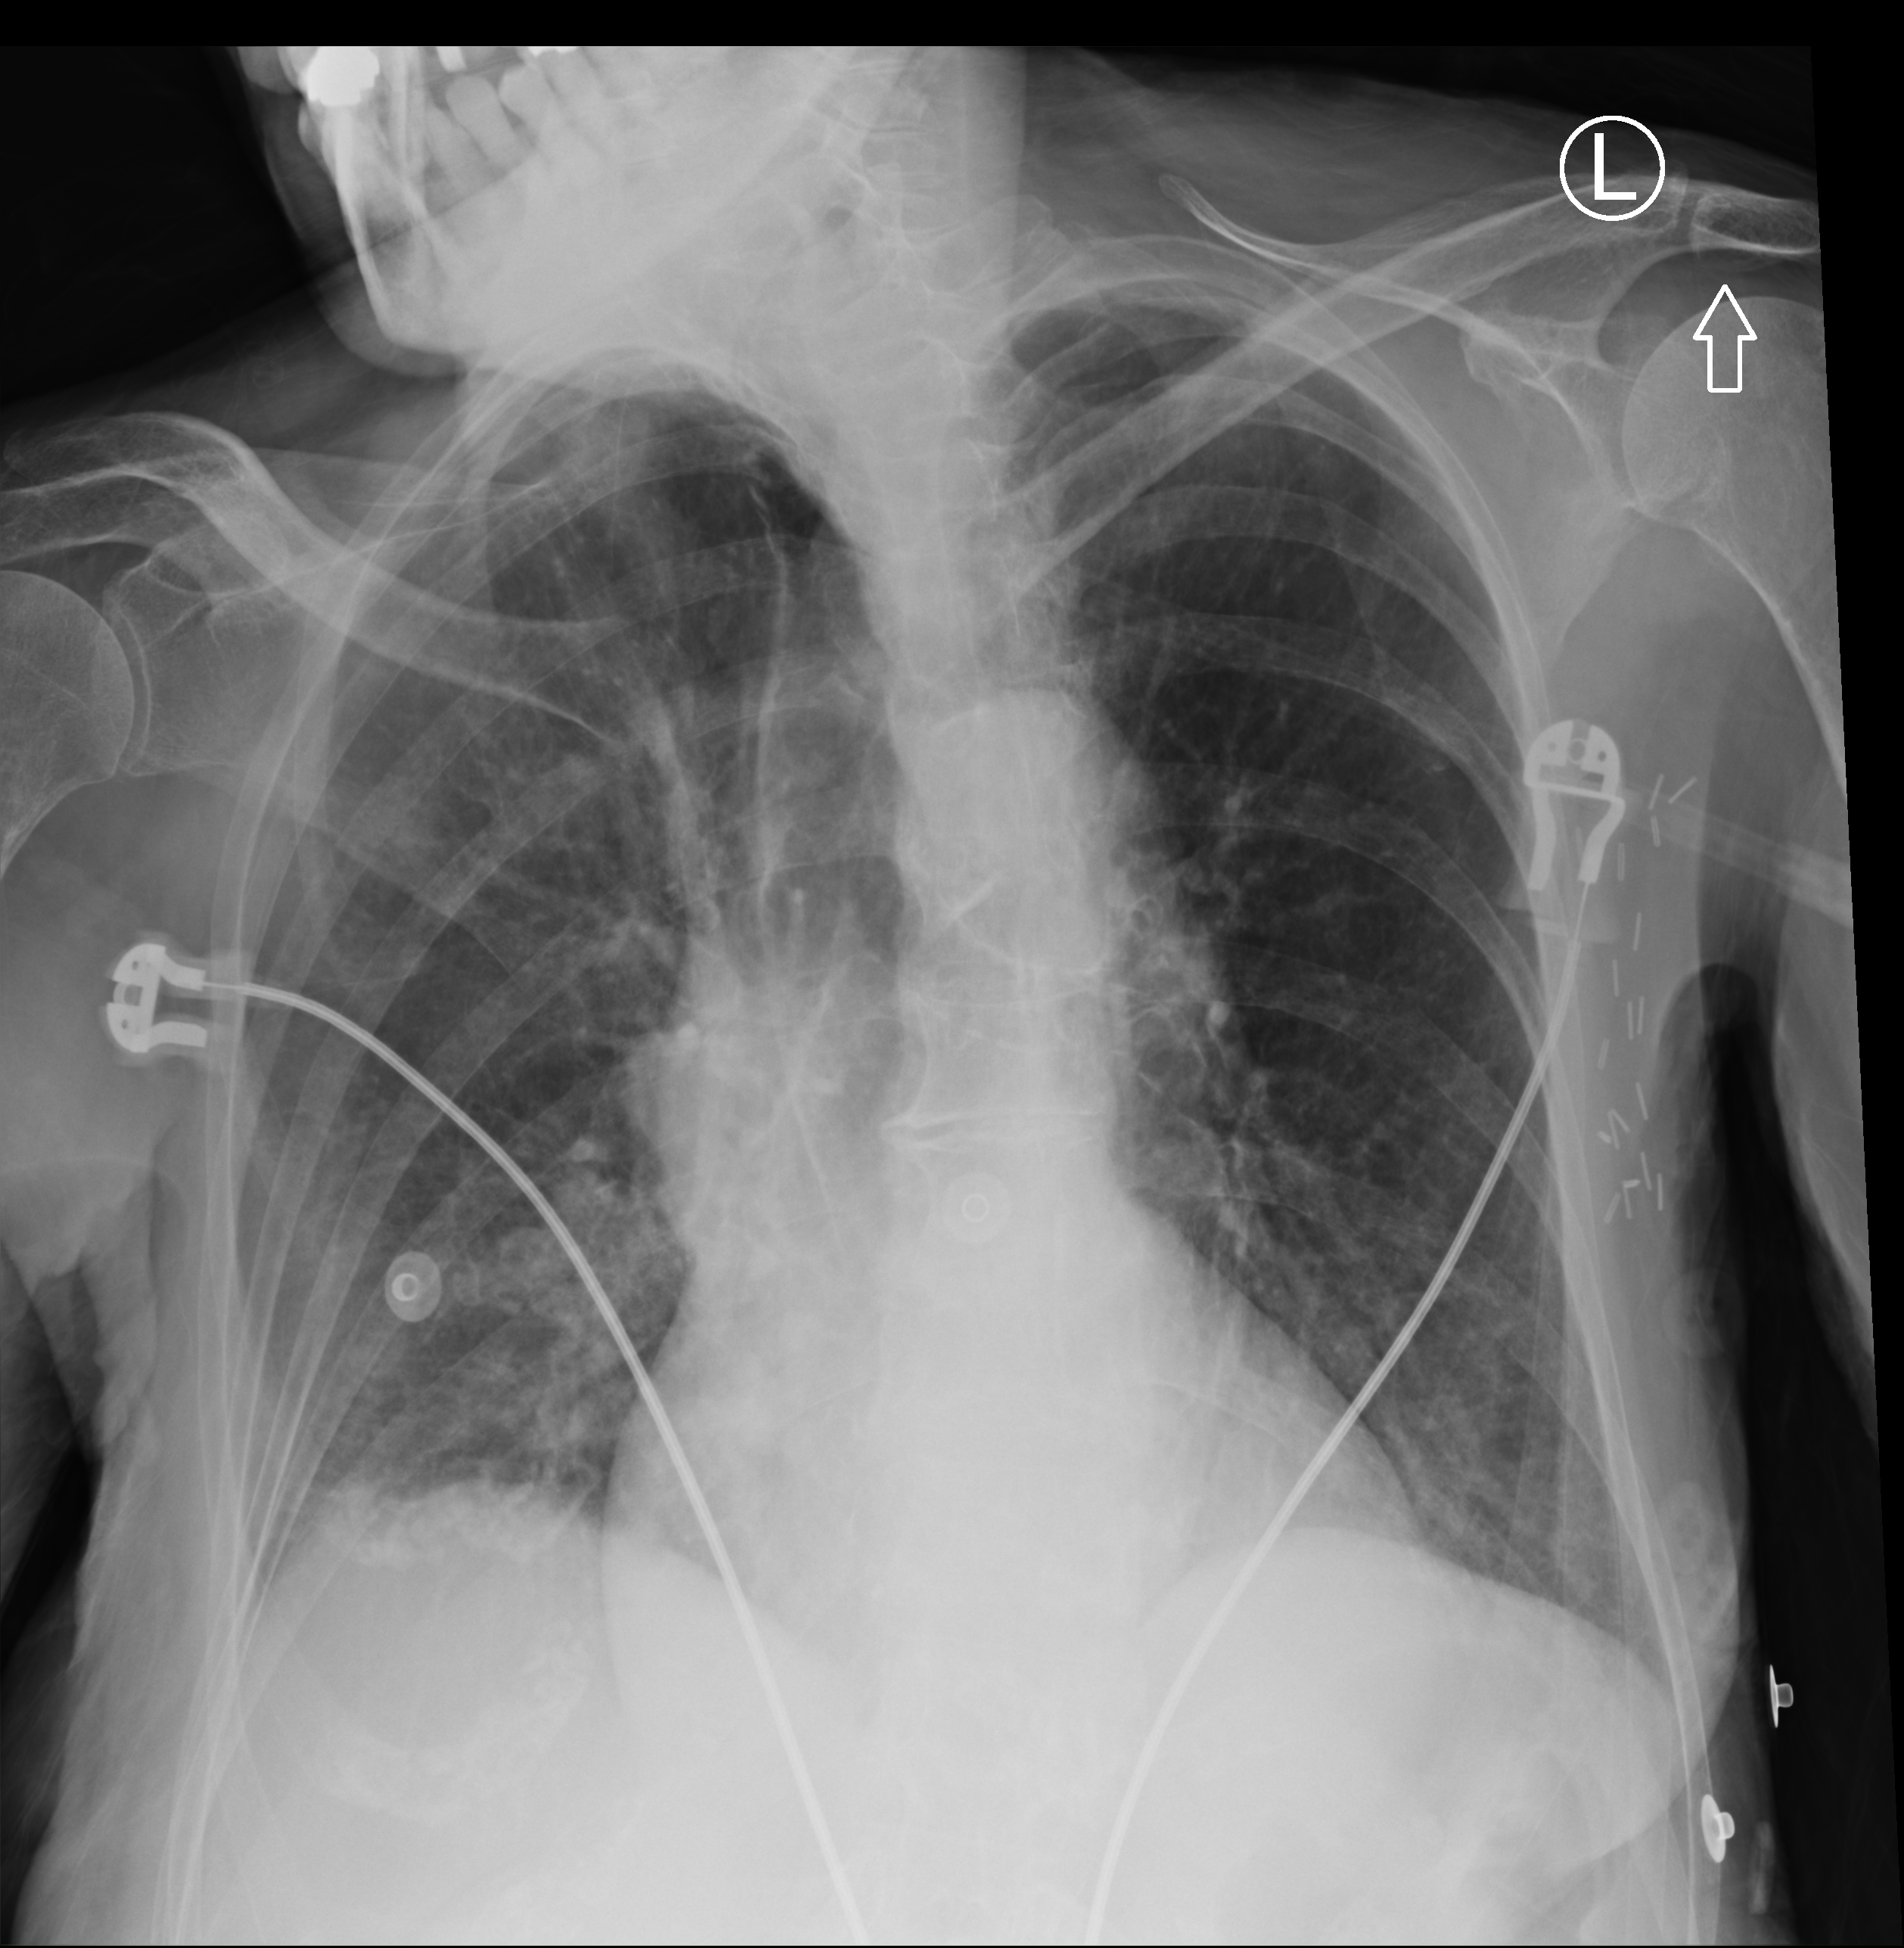
Chest X-ray (portable), anteroposterior (AP) projection. Female patient hospitalised with COVID-19, age 75–90 years.
Admission-level facts for this patient (not findings on this image; timing relative to this image not recorded):
- admitted to intensive care during this hospital stay: no
- mechanically ventilated during this hospital stay: no